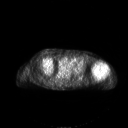
FDG PET of an extremity soft-tissue mass (from a PET/CT study), one axial slice; slice 152 of 267 in the series (ordered by position); 128 × 128 image matrix. Female patient, age 83 years. From the clinical record (not read from this slice): histological type: pleiomorphic leiomyosarcoma; grade: high; site of the primary tumour: left biceps.
Annotated regions visible in this slice (expert contour drawn on MRI and transferred to this co-registered scan by the dataset authors):
- gross tumour volume including surrounding oedema: bounding box (x1, y1, x2, y2) in pixels: (91, 62, 108, 77)
- gross tumour volume (mass): (91, 62, 108, 77)